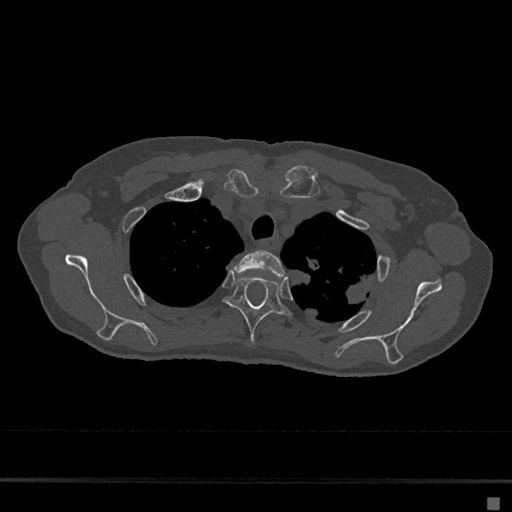
CT including the spine, one axial slice; slice 545 of 797 in the series (ordered by position); reconstruction kernel Br40s/3; 120 kVp; bone window (W 1800 / L 400 HU); 0.5 mm slice thickness; 512 × 512 image matrix, field of view 360 × 360 mm. Female patient, age 68 years. From the clinical record (not read from this slice): primary cancer: renal.
Annotated regions visible in this slice (semi-automatic segmentation, software-assisted and operator-edited):
- T2 vertebra: bounding box (x1, y1, x2, y2) in pixels: (233, 250, 285, 278)
- T3 vertebra: (224, 277, 289, 345)